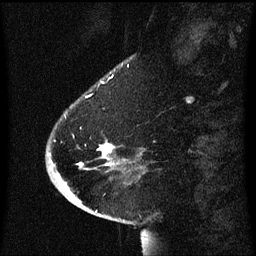
Breast MRI (dynamic contrast-enhanced), one sagittal slice. Slice 15 of 60 in the series (ordered by position). Dynamic contrast-enhanced series, image 2 of 3 at this slice position (ordered by acquisition). 1.5 T. TE 4.2 ms, TR 8.4 ms. 2 mm slice thickness. 256 × 256 image matrix, field of view 200 × 200 mm. Patient: female, 54 years. From the clinical record (not read from this slice): setting: breast cancer imaged before/during neoadjuvant chemotherapy; receptor status: HR-positive, HER2-negative.
Outlined on this slice (semi-automatically segmented with operator editing):
- analysis volume of interest (the breast-tissue region the enhancement analysis was run in; not a lesion): bounding box [x1, y1, x2, y2] px = [46, 106, 122, 171]
- tumour enhancement mask (voxels above the 70 % enhancement threshold inside the analysis volume of interest): [101, 146, 114, 153]